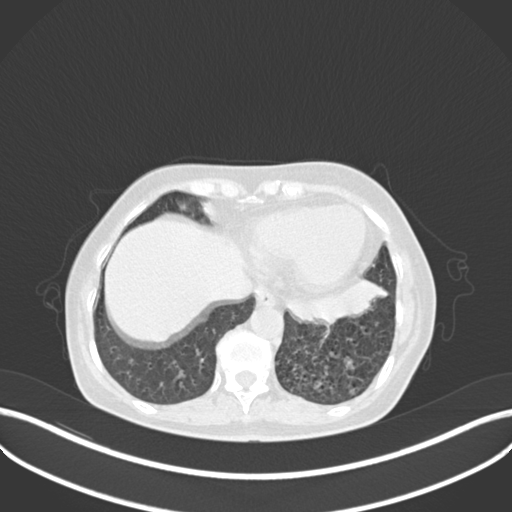
Chest CT, one axial slice; position 60 of 270 along the scan axis; 120 kVp; lung window (W 1500 / L -600 HU); 1 mm slice thickness; 512 × 512 image matrix, field of view 400 × 400 mm. Female patient, age 63 years. From the clinical record (not read from this slice): clinical TNM (as recorded): T1b N0 M0.
Outlined on this slice (bounding box drawn by a radiologist):
- lung tumour (recorded histology: adenocarcinoma): box from (x=283, y=280) to (x=398, y=323) px